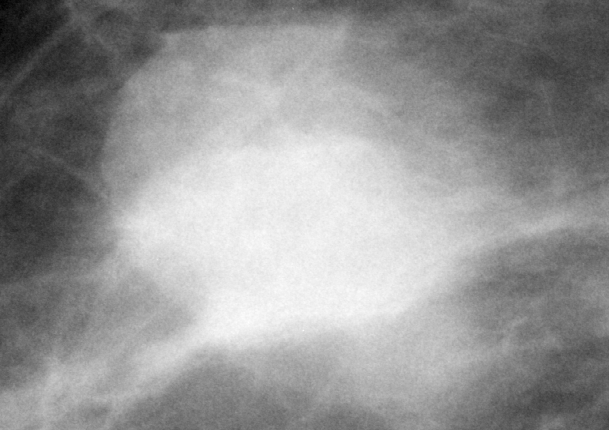
Region of interest cut from a scanned film mammogram (one marked finding); right breast; MLO view; BI-RADS breast density category 1 (scale 1–4).
Marked abnormality: mass, shape lobulated, margins circumscribed; BI-RADS assessment category 5; subtlety rating 5 on a 1 (subtle) to 5 (obvious) scale; pathology (as recorded): malignant.